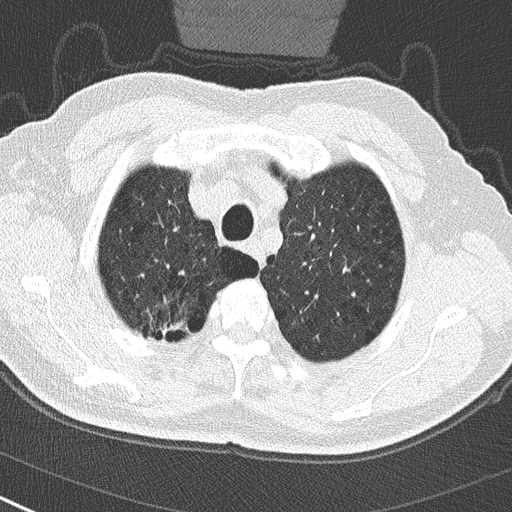
Low-dose screening chest CT, one axial slice. Position 244 of 290 along the scan axis. Reconstruction kernel B50f. 120 kVp. Lung window (W 1500 / L -600 HU). 512 × 512 image matrix, field of view 300 × 300 mm.
Outlined on this slice (outlined manually by an expert reader):
- lesion 1 (tumor, upper lobe of right lung): box from (x=154, y=309) to (x=187, y=337) px